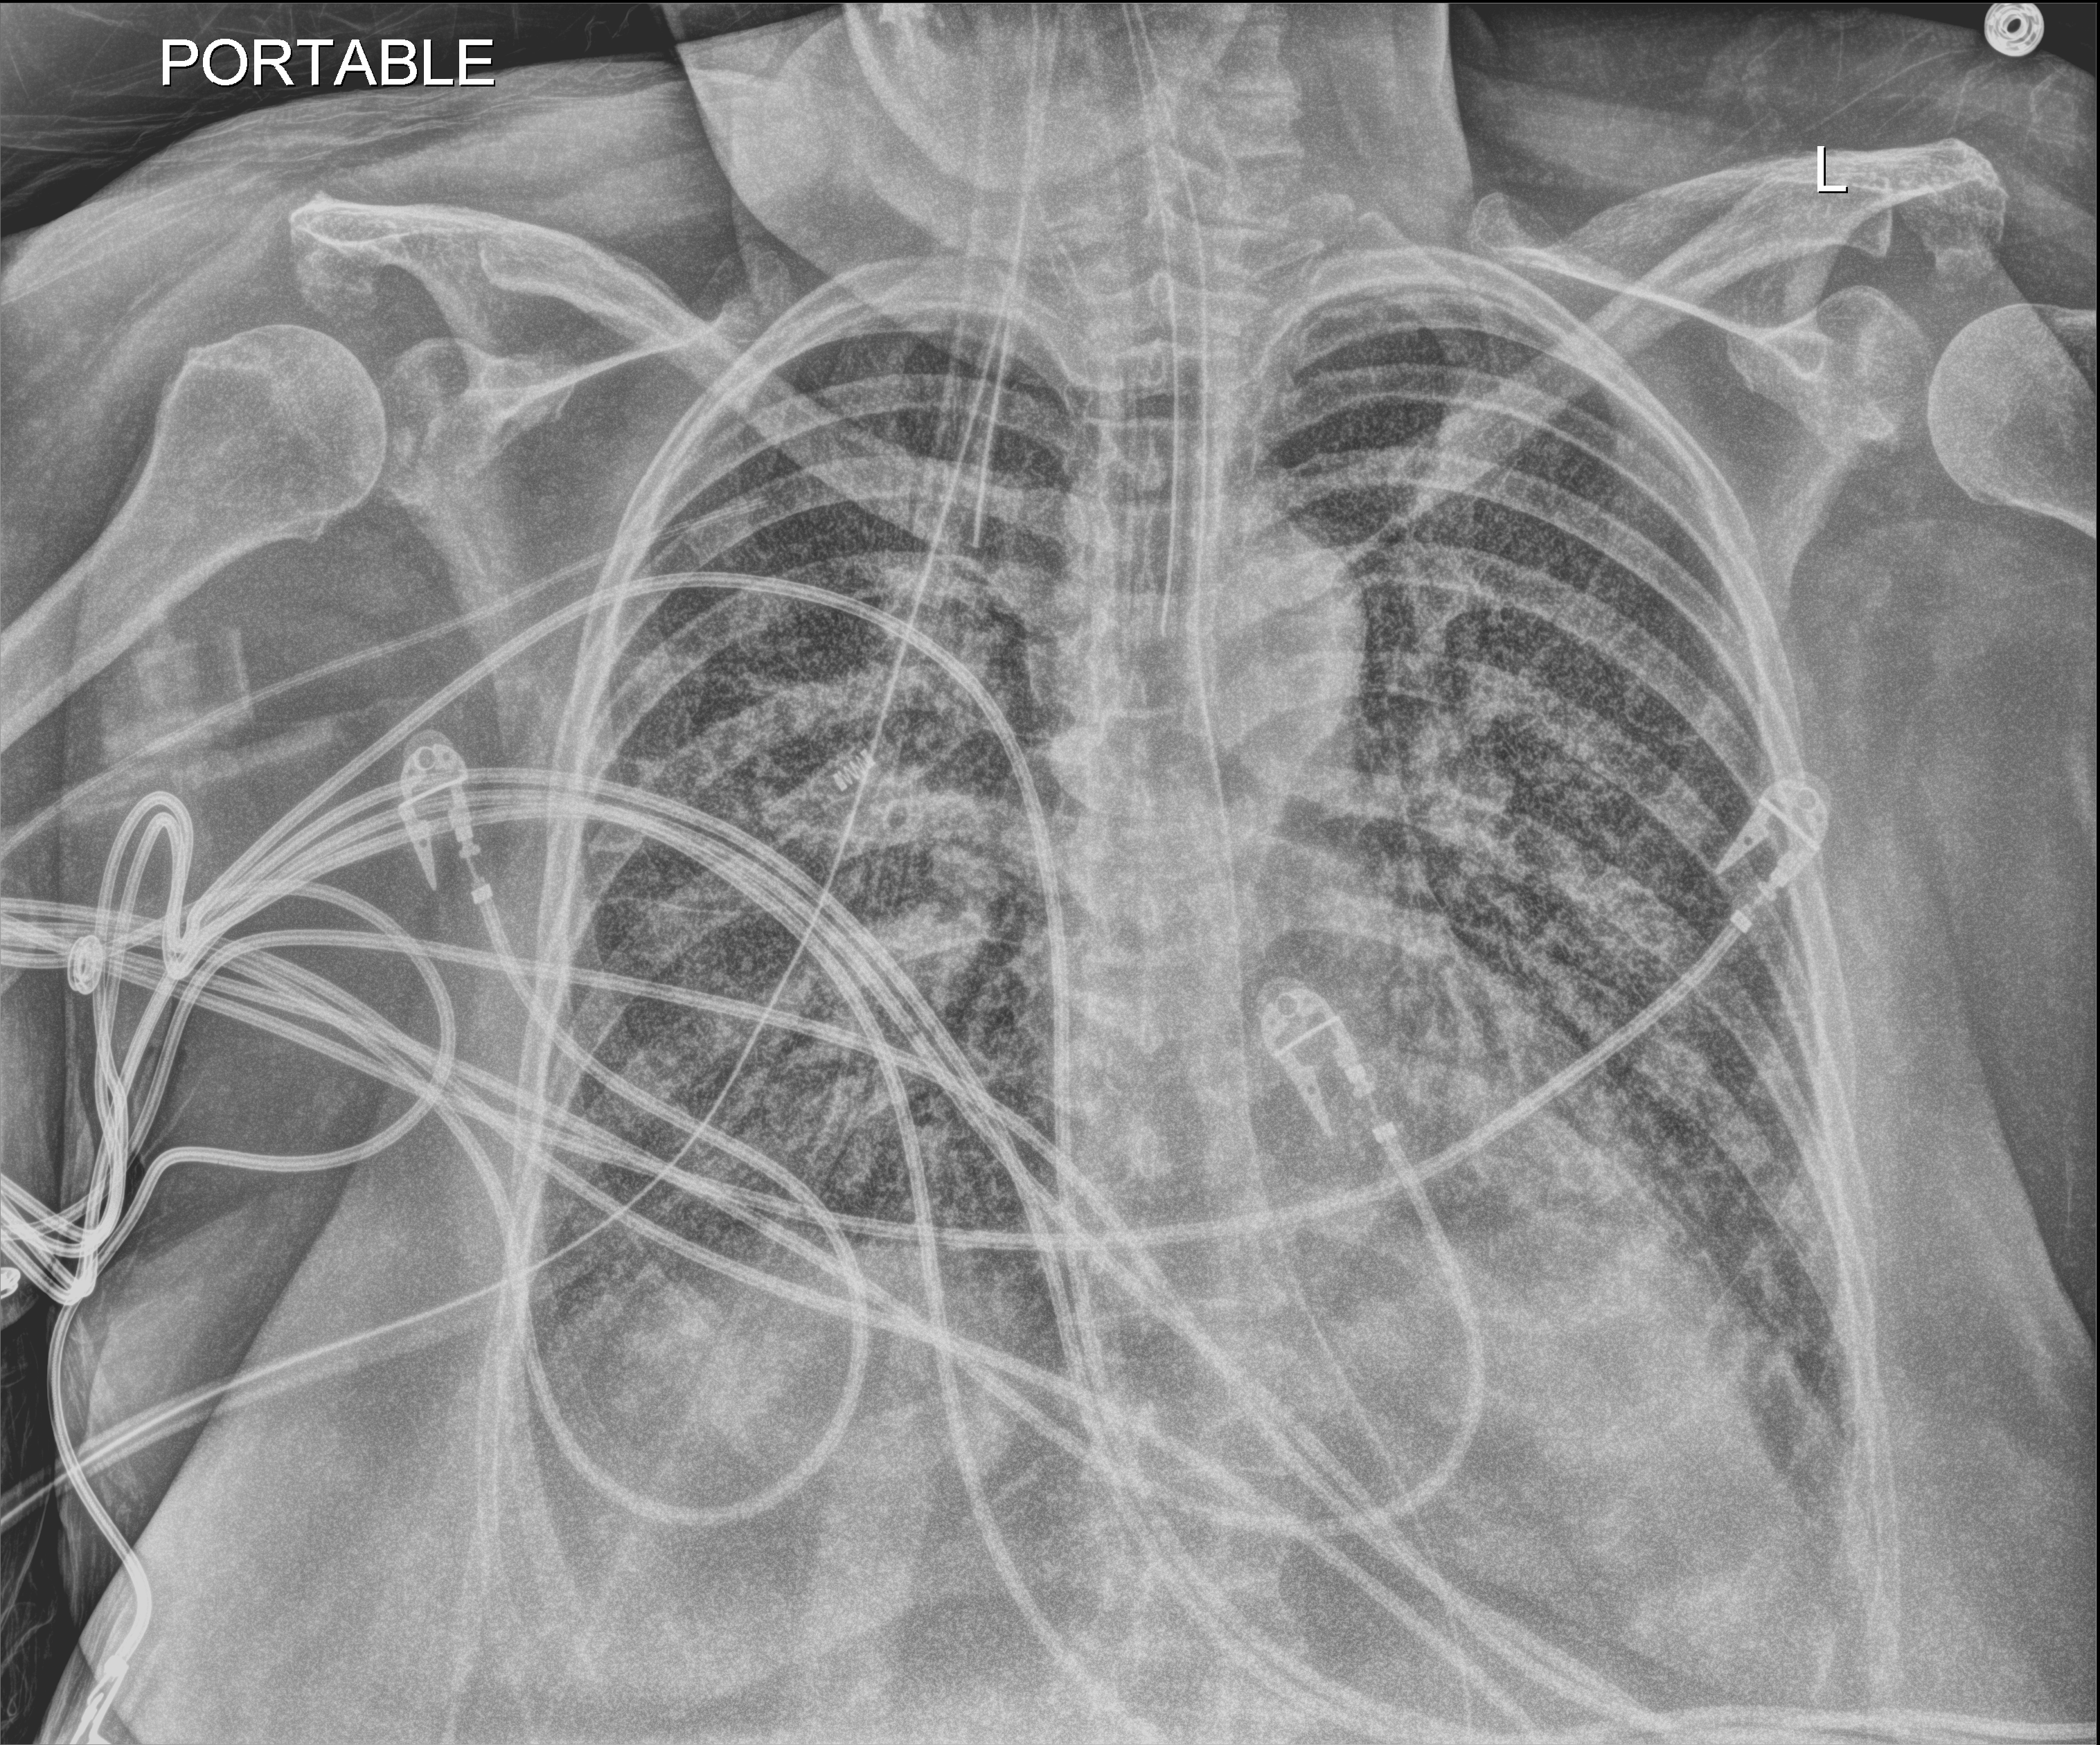
Bedside chest radiograph (digital radiography); anteroposterior (AP) projection. Patient hospitalised with COVID-19; female, aged 60–74 years.
From the hospital-stay record, not from the radiograph (when in the stay this image was taken is not recorded): chronic kidney disease (admission record): no.